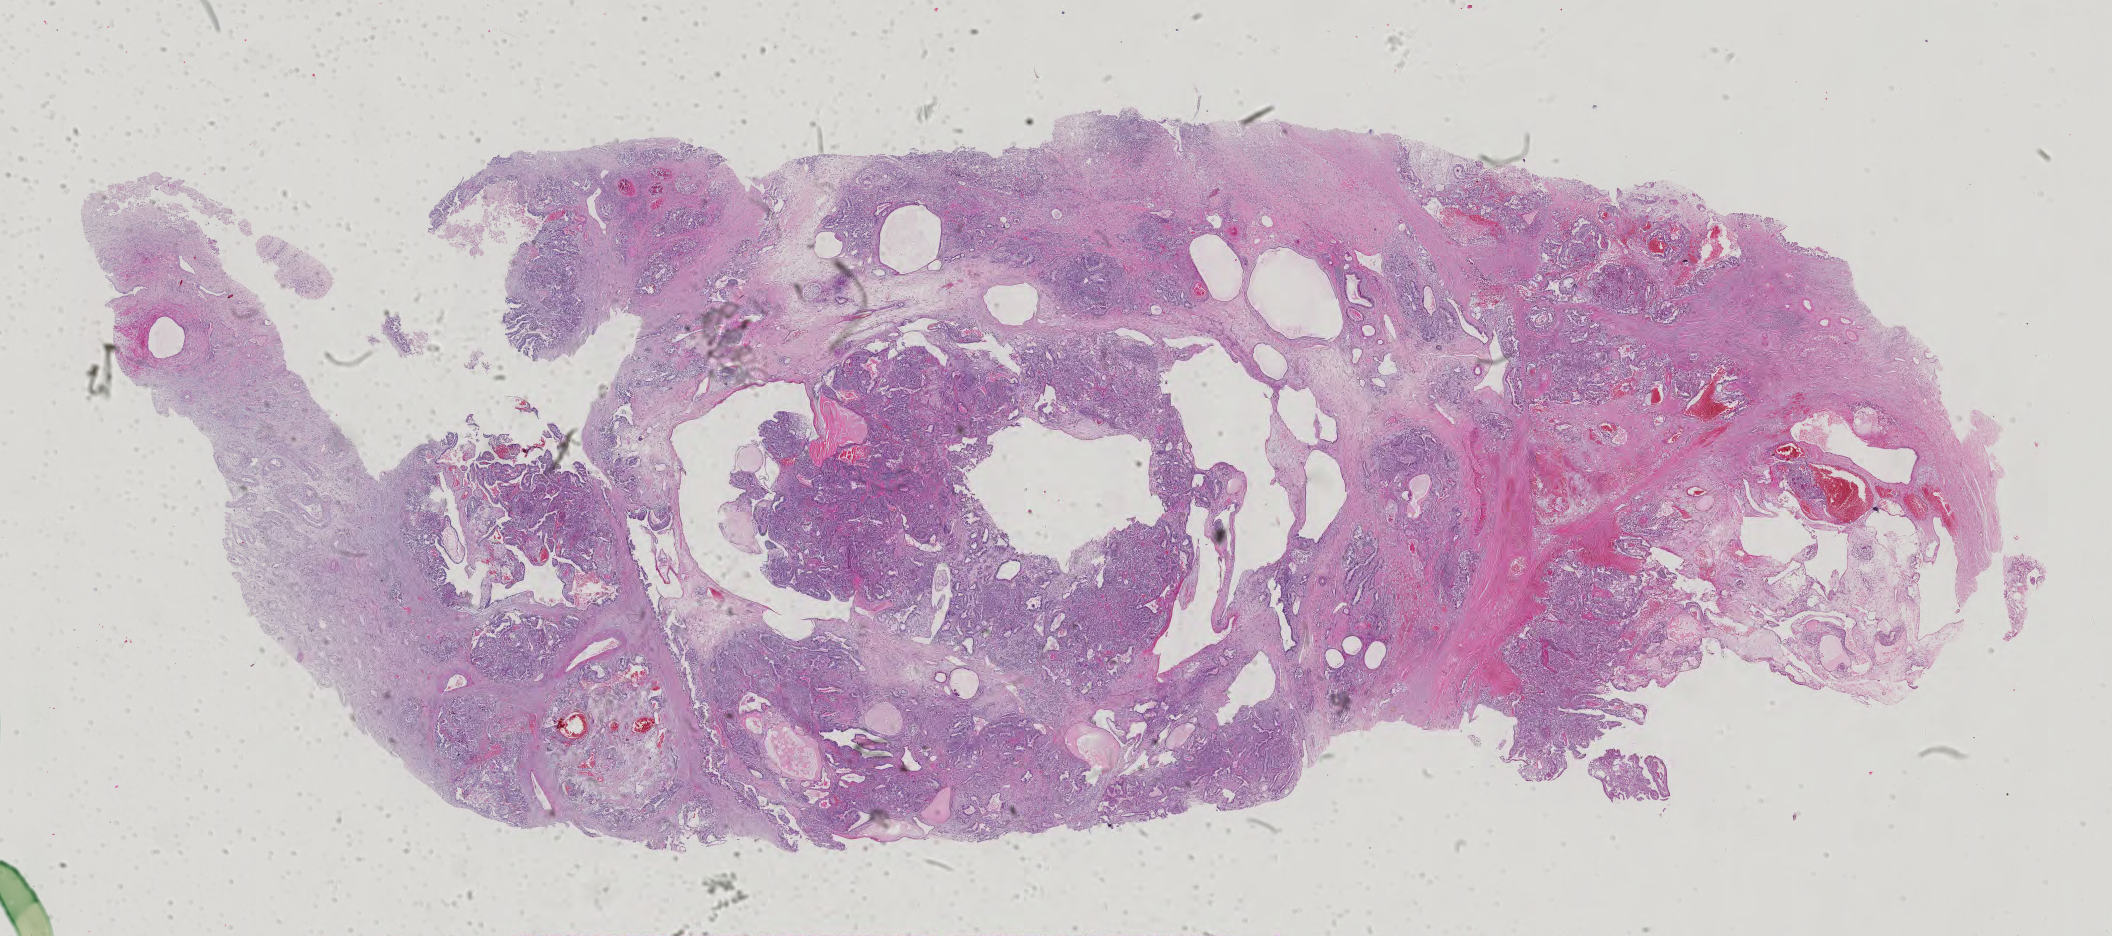
Whole-slide histology image, Hematoxylin and eosin (H&E) stained, low-resolution overview of the scanned area, about 30.8 x 13.6 mm (slide scanned at 40x). Formalin-fixed paraffin-embedded (FFPE) diagnostic section. Primary tumour sample from the testis. Patient: male, age at initial diagnosis 51 years.
* histologic diagnosis: Yolk sac tumor
* AJCC pathologic stage: IS (6th edition)
* TNM: T2 N0 M0